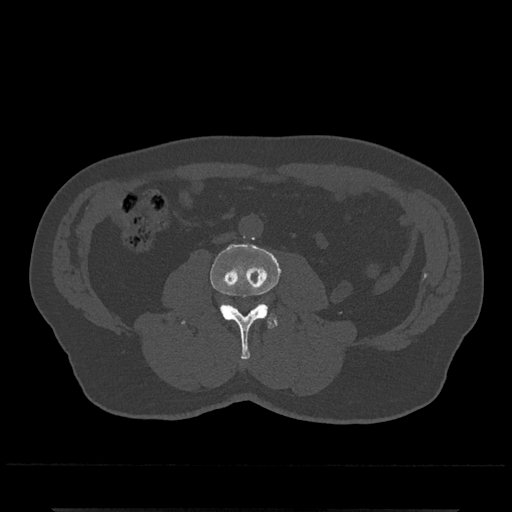
CT including the spine, one axial slice. Slice 212 of 797 in the series (ordered by position). 120 kVp. Bone window (W 1800 / L 400 HU). 0.5 mm slice thickness. 512 × 512 image matrix, field of view 393 × 393 mm. Male patient, age 67 years. From the clinical record (not read from this slice): primary cancer: prostate.
Structures marked on this image (semi-automatic segmentation, software-assisted and operator-edited):
- L3 vertebra: bounding box (x1, y1, x2, y2) in pixels: (181, 244, 281, 360)
- L4 vertebra: (263, 303, 278, 325)